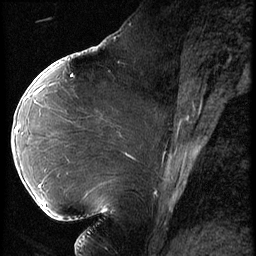
Breast MRI (dynamic contrast-enhanced), one sagittal slice; position 29 of 62 along the scan axis; 3 images stored at this slice position (order not interpretable as contrast timing); 1.5 T; TE 4.2 ms, TR 9 ms; 2.5 mm slice thickness; 256 × 256 image matrix, field of view 180 × 180 mm. Patient: female, 43 years. Case-level facts recorded for this patient, not image findings: setting: breast cancer imaged before/during neoadjuvant chemotherapy; receptor status: HER2-positive.
Structures marked on this image (semi-automatically segmented with operator editing):
- analysis volume of interest (the breast-tissue region the enhancement analysis was run in; not a lesion): box from (x=12, y=90) to (x=82, y=203) px
- tumour enhancement mask (voxels above the 140 % enhancement threshold inside the analysis volume of interest): (x=16, y=92)–(x=38, y=133)